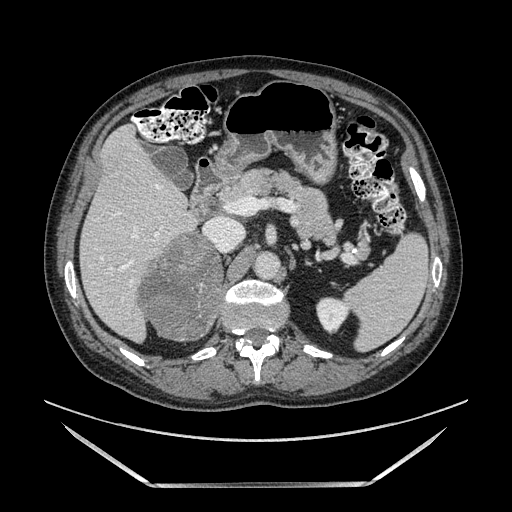
Contrast-enhanced abdominal CT, one axial slice. Slice 82 of 185 in the series (ordered by position). Soft-tissue window (W 400 / L 40 HU). 1.25 mm slice thickness. 512 × 512 image matrix. Male patient. Case-level facts recorded for this patient, not image findings: diagnosis: adrenocortical carcinoma; tumour side: right adrenal.
Structures marked on this image (semi-automatic segmentation, software-assisted and operator-edited):
- mass: box from (x=140, y=235) to (x=222, y=337) px